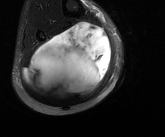
MRI of an extremity soft-tissue mass, one axial slice; position 67 of 81 along the scan axis; T2-weighted fat-saturated; MR volume resampled by the dataset authors to the PET/CT grid (not the native acquisition matrix); 3.27 mm slice thickness; 165 × 137 image matrix, field of view 161 × 134 mm. Male patient. From the clinical record (not read from this slice): histological type: liposarcoma - round cell; grade: high; site of the primary tumour: right calf.
Annotated regions visible in this slice (expert contour drawn on MRI and transferred to this co-registered scan by the dataset authors):
- gross tumour volume (mass): bounding box (x1, y1, x2, y2) in pixels: (23, 21, 111, 97)